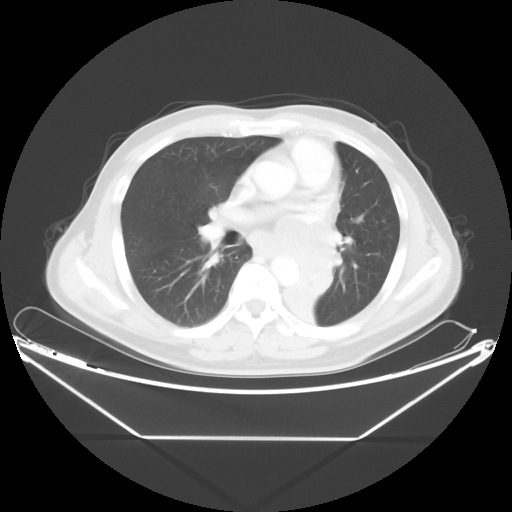
Chest CT, one axial slice. Slice 25 of 48 in the series (ordered by position). Reconstruction kernel STANDARD. 120 kVp. Lung window (W 1500 / L -600 HU). 5 mm slice thickness. 512 × 512 image matrix, field of view 438 × 438 mm. Patient: male, 58 years. Case-level facts recorded for this patient, not image findings: clinical TNM (as recorded): T3 N3 M0.
Annotated regions visible in this slice (rectangle marked by the reading radiologist):
- lung tumour (recorded histology: squamous cell carcinoma): bounding box [x1, y1, x2, y2] px = [284, 237, 352, 333]